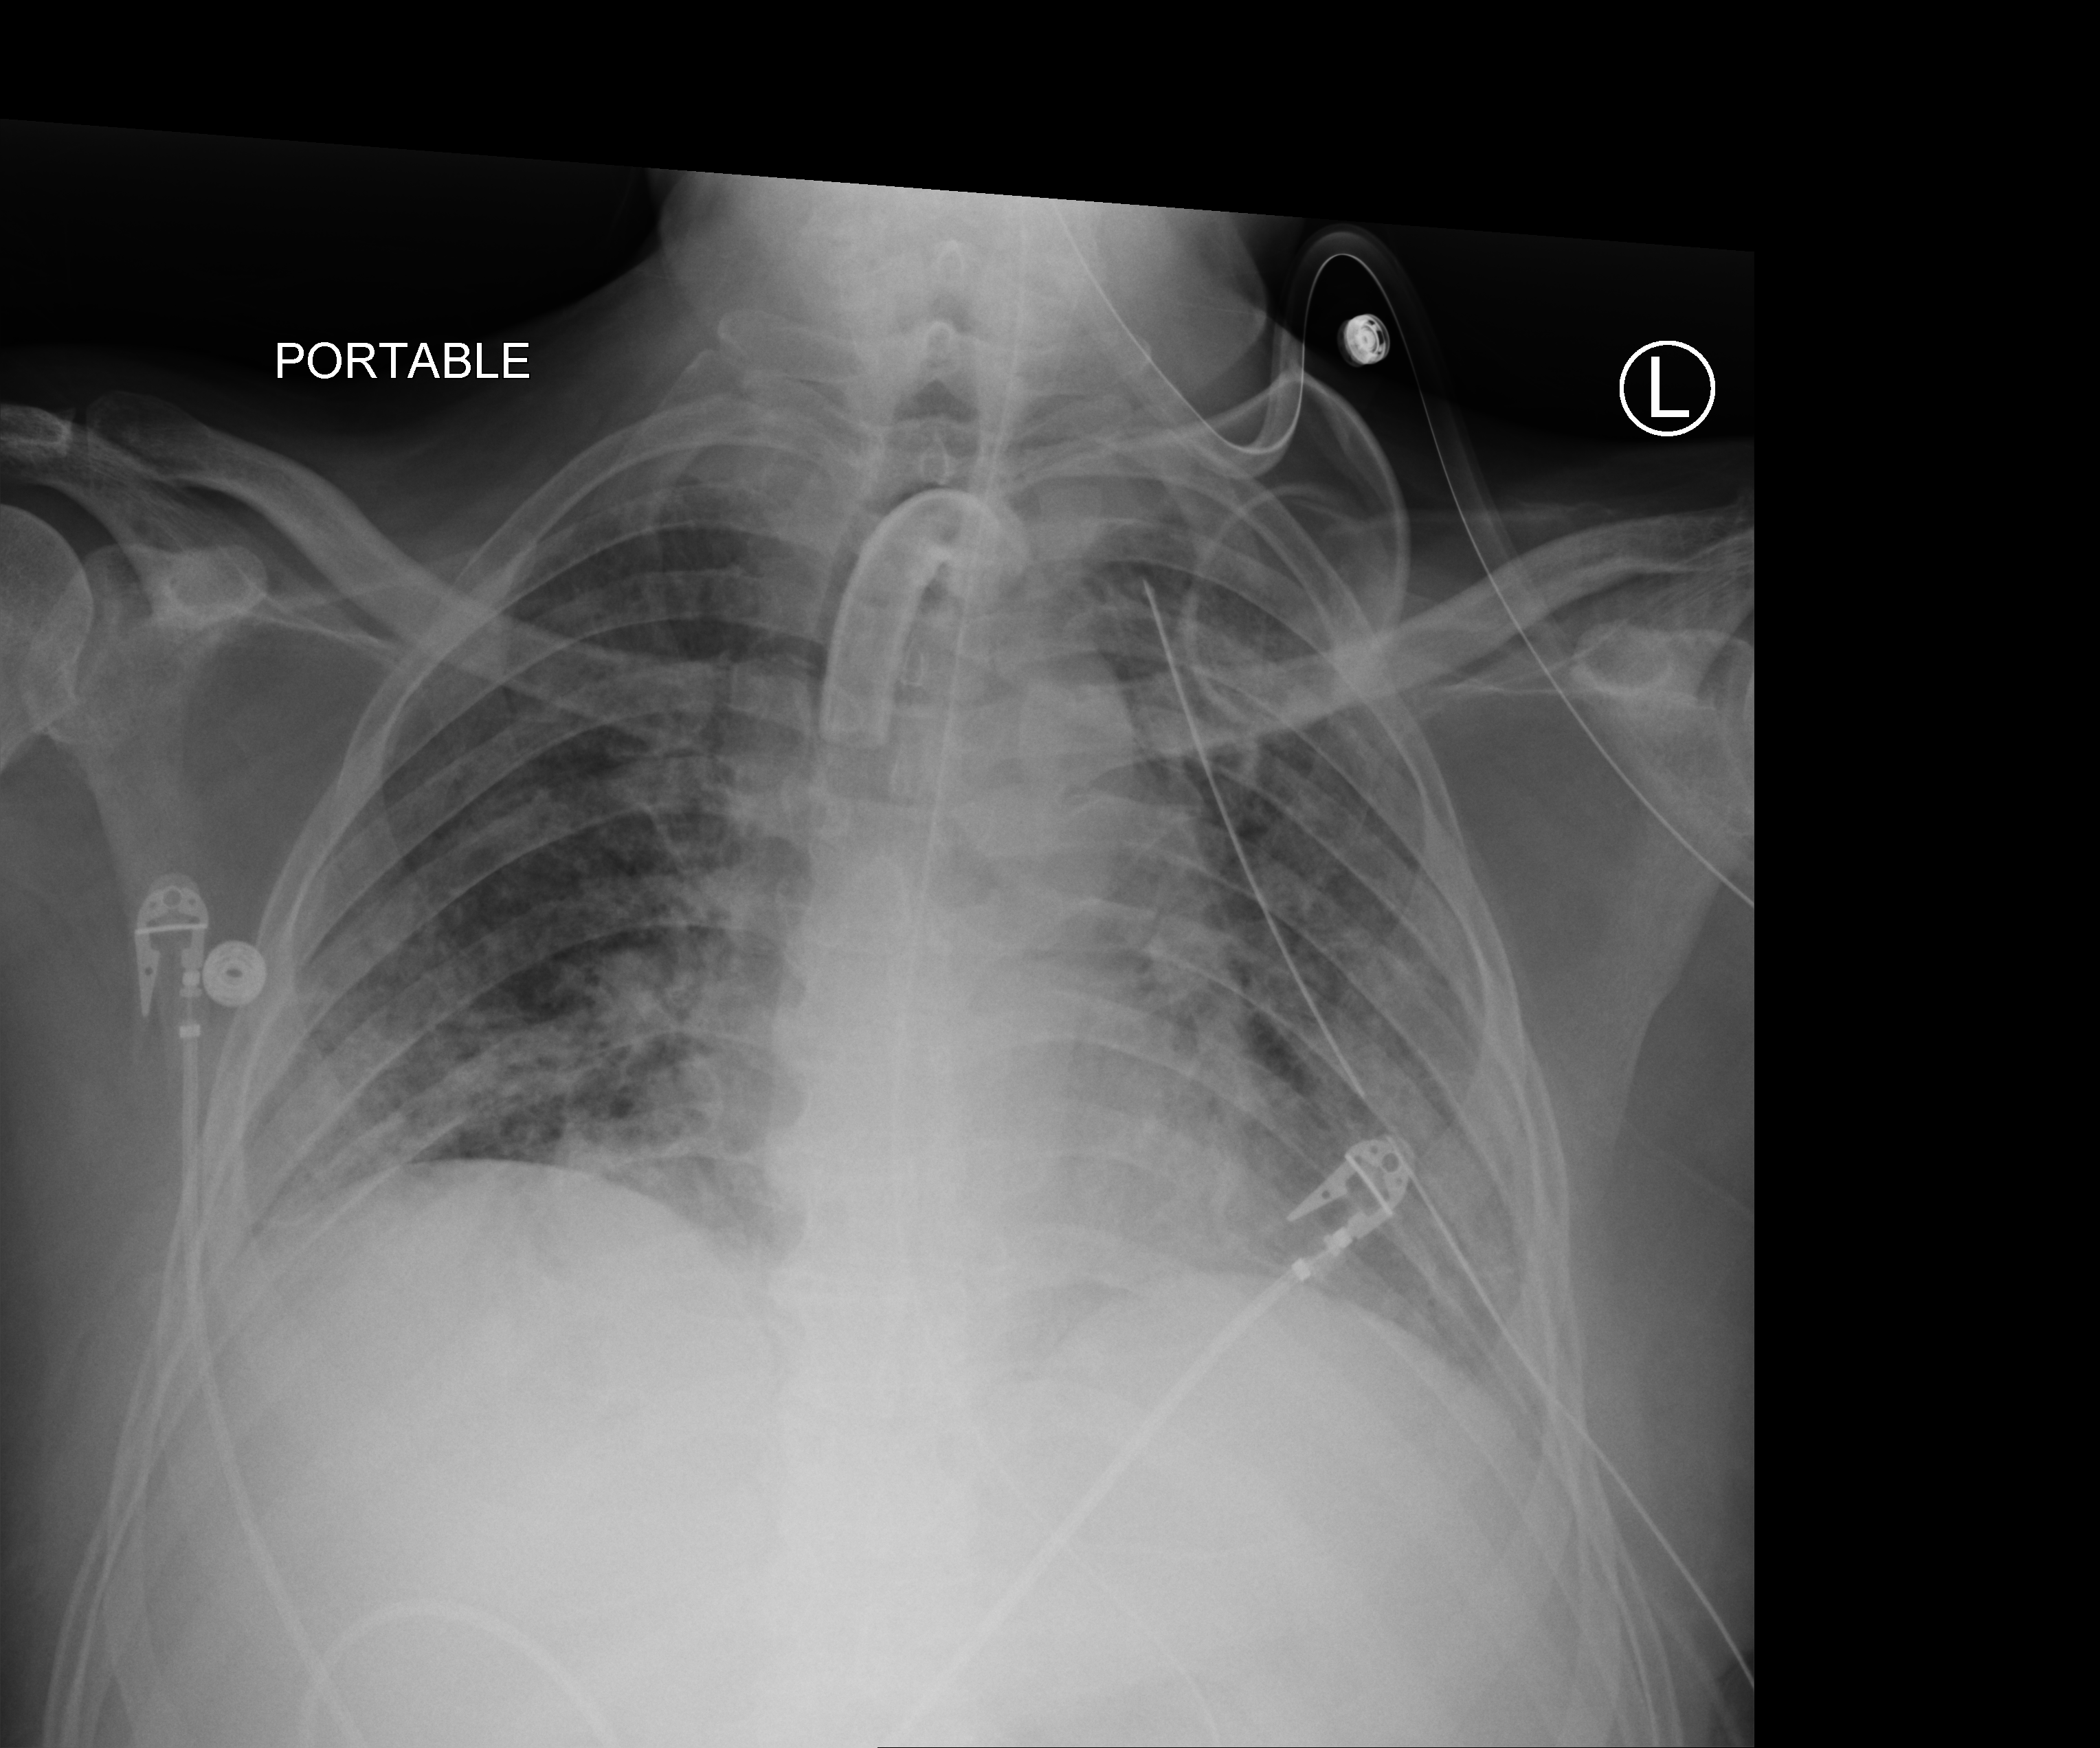
Bedside chest radiograph (computed radiography); anteroposterior (AP) projection. Patient hospitalised with COVID-19; male, aged 18–59 years.
Hospital-stay facts (about this admission, not read from this image; timing relative to this image not recorded):
- mechanically ventilated during this hospital stay: yes
- admitted to intensive care during this hospital stay: yes